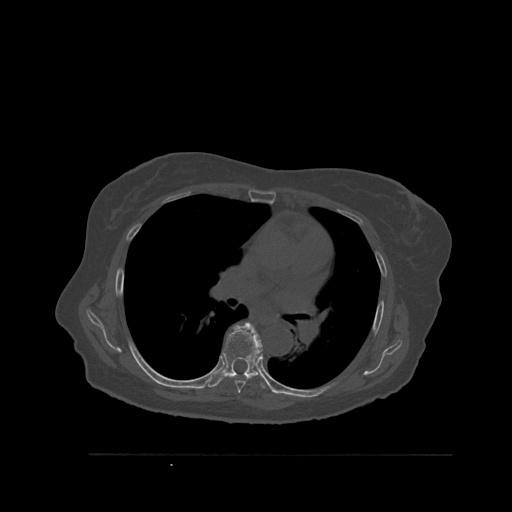
CT including the spine, one axial slice. Slice 372 of 527 in the series (ordered by position). Bone window (W 1800 / L 400 HU). 512 × 512 image matrix. Patient: female, 73 years. From the clinical record (not read from this slice): primary cancer: breast.
Annotated regions visible in this slice (semi-automatically segmented with operator editing):
- T6 vertebra: bounding box (x1, y1, x2, y2) in pixels: (235, 358, 258, 393)
- T7 vertebra: (207, 322, 268, 390)